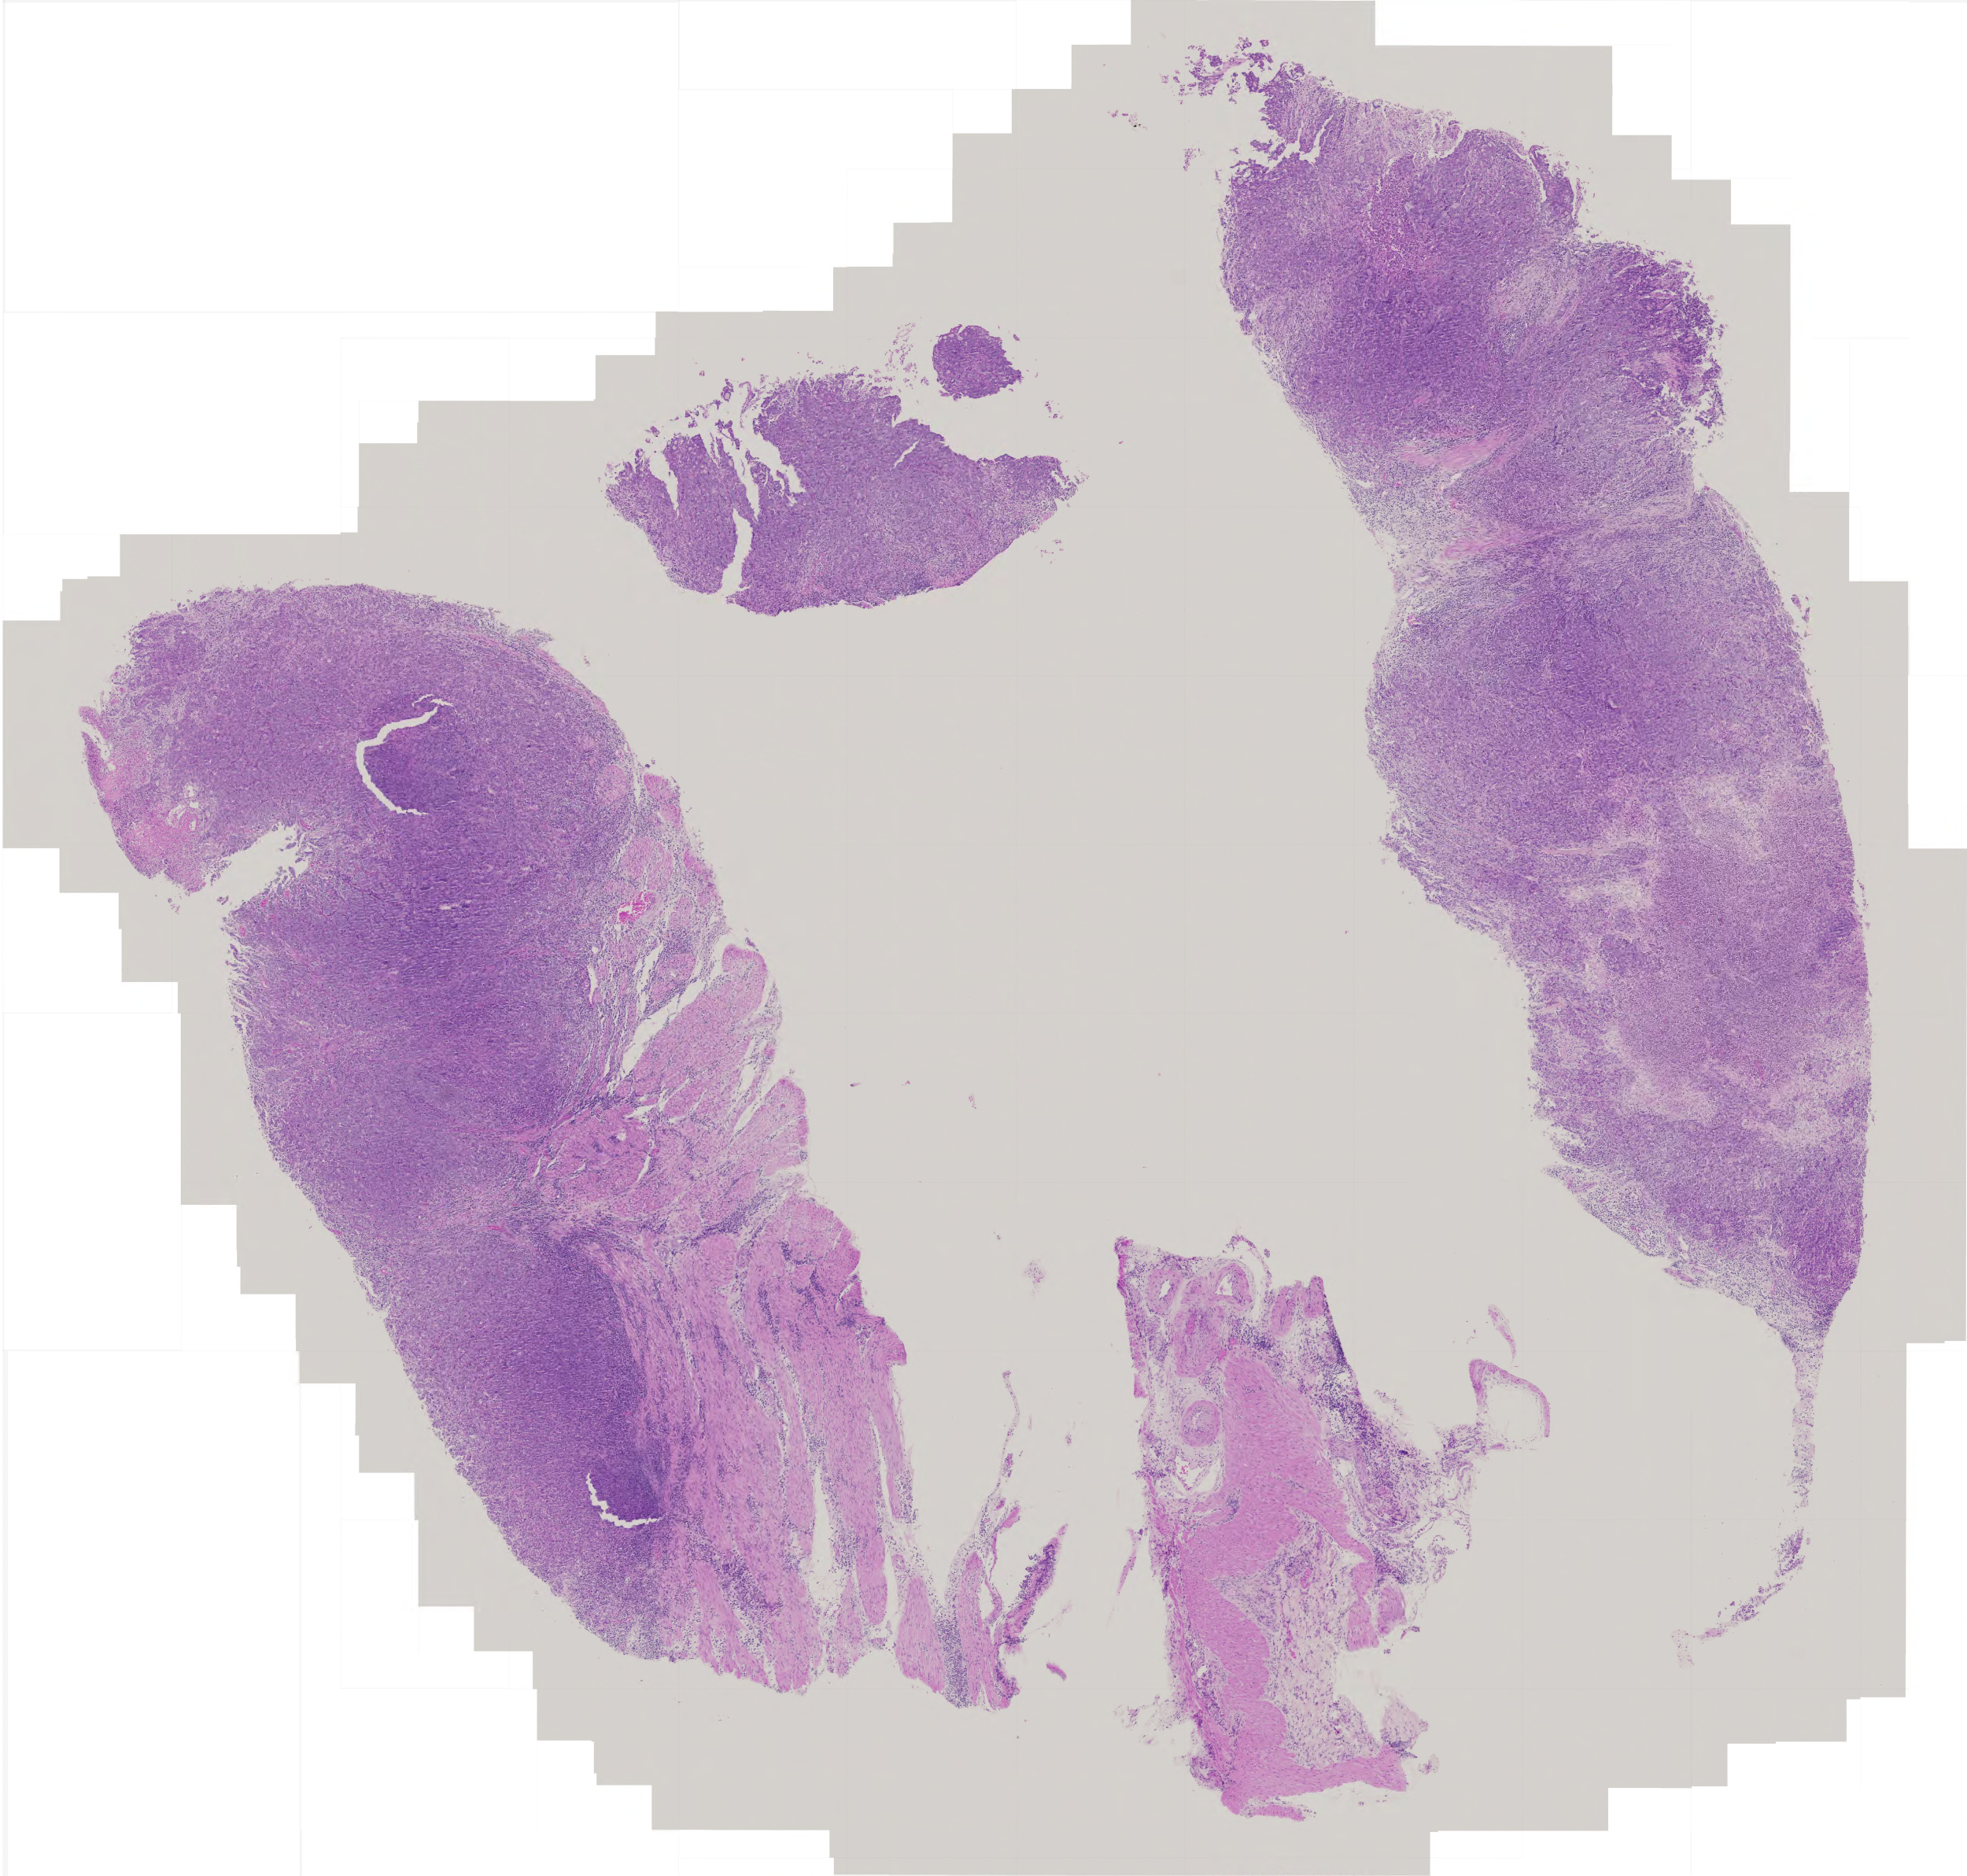
H&E-stained whole-slide image, low-resolution overview of the scanned area, about 5.0 x 4.8 mm. Formalin-fixed paraffin-embedded (FFPE) diagnostic section. Primary tumour sample from the stomach. Patient sex: male.
Histologic diagnosis: Adenocarcinoma, NOS (cardia, NOS).